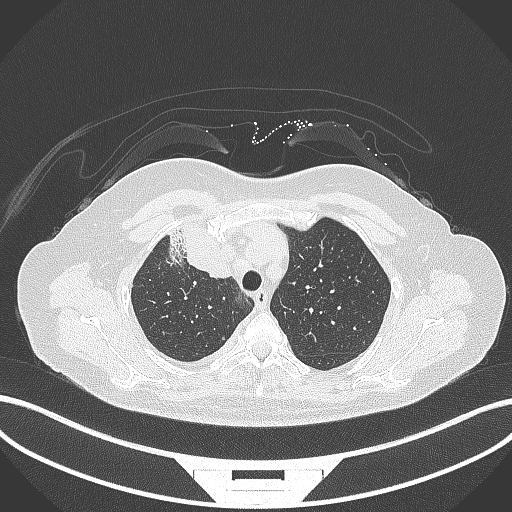
Chest CT, one axial slice; position 241 of 305 along the scan axis; reconstruction kernel B70f; 120 kVp; lung window (W 1500 / L -600 HU); 1 mm slice thickness; 512 × 512 image matrix. Patient: female, 52 years. From the clinical record (not read from this slice): clinical TNM (as recorded): T3 N1 M1.
Annotated regions visible in this slice (bounding box drawn by a radiologist):
- lung tumour (recorded histology: adenocarcinoma): bounding box (x1, y1, x2, y2) in pixels: (165, 226, 236, 279)